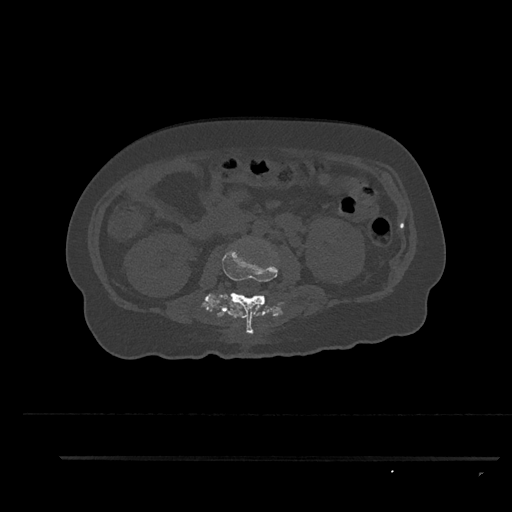
CT including the spine, one axial slice. Position 137 of 797 along the scan axis. Bone window (W 1800 / L 400 HU). 512 × 512 image matrix, field of view 408 × 408 mm. Patient: female, 44 years. Case-level facts recorded for this patient, not image findings: primary cancer: renal.
Annotated regions visible in this slice (semi-automatically segmented with operator editing):
- L2 vertebra: box from (x=222, y=249) to (x=278, y=335) px